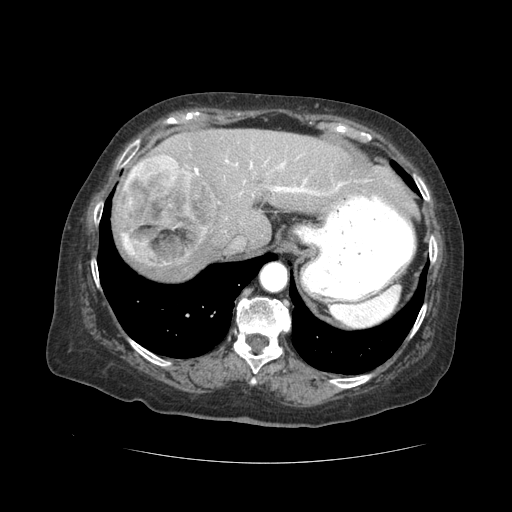
Contrast-enhanced abdominal CT (liver protocol), one axial slice. Slice 35 of 59 in the series (ordered by position). 120 kVp. Soft-tissue window (W 400 / L 40 HU). 2.5 mm slice thickness. 512 × 512 image matrix. From the clinical record (not read from this slice): diagnosis: hepatocellular carcinoma (patient treated with transarterial chemoembolisation; whether this scan precedes or follows treatment is not stated here); TNM stage (as recorded): Stage-I; Child-Pugh class: A; tumour nodularity: uninodular.
Structures marked on this image (semi-automatically segmented with operator editing):
- abdominal aorta: box from (x=261, y=264) to (x=287, y=291) px
- liver parenchyma outside the tumour (the mass and vessels are separate outlines, so this box may not span the whole liver): (x=112, y=128)–(x=406, y=280)
- mass: (x=118, y=154)–(x=216, y=267)
- liver vessels: (x=194, y=155)–(x=367, y=196)